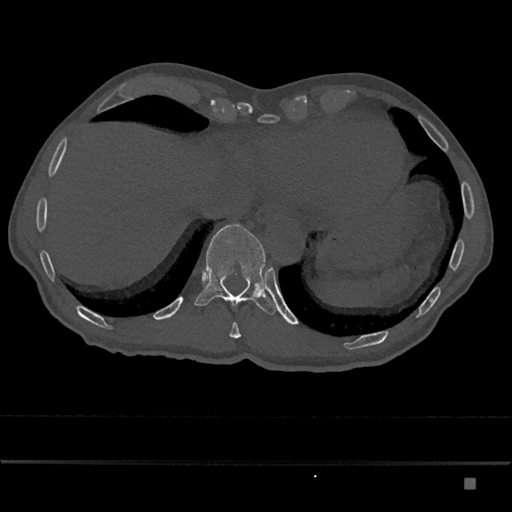
CT including the spine, one axial slice. 120 kVp. Bone window (W 1800 / L 400 HU). 512 × 512 image matrix, field of view 390 × 390 mm. Male patient, age 72 years. Case-level facts recorded for this patient, not image findings: primary cancer: prostate.
Structures marked on this image (semi-automatically segmented with operator editing):
- T10 vertebra: bounding box <229,322,241,339> (left, top, right, bottom; pixels)
- T11 vertebra: <193,224,276,315>